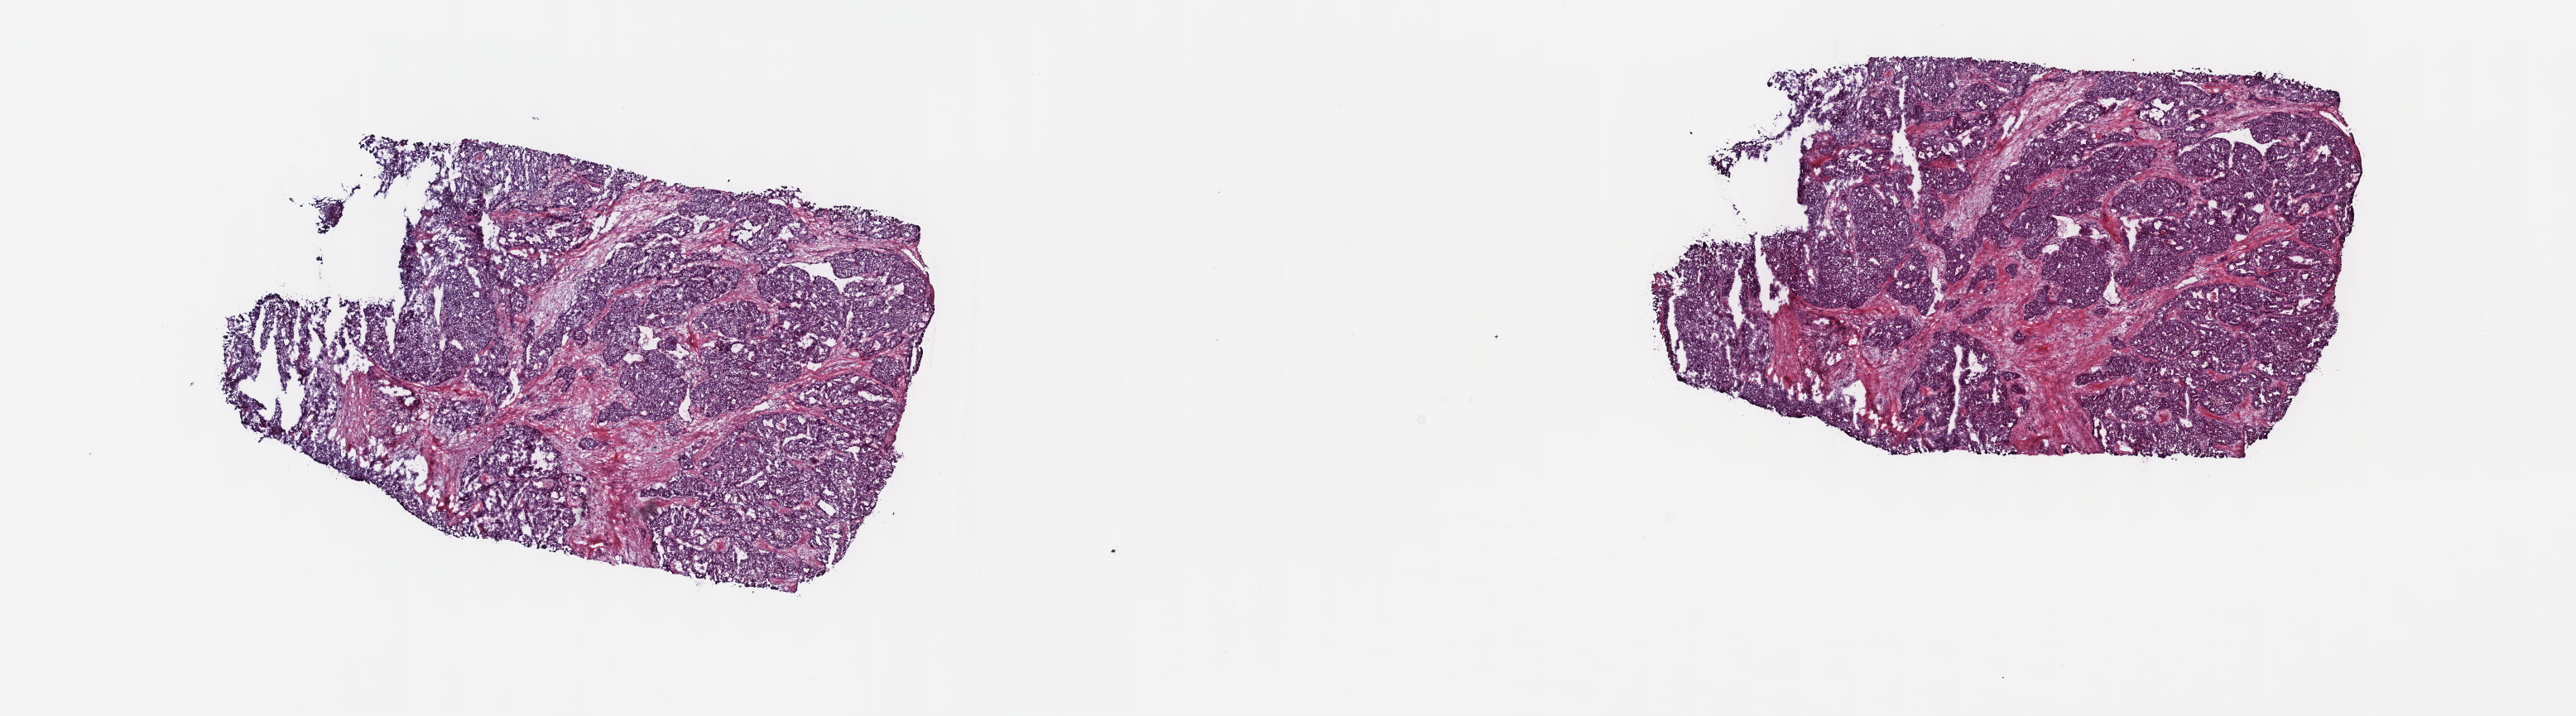
Digitized Hematoxylin and eosin (H&E) stained tissue section (whole slide), shown as a low-resolution overview of the whole scanned area (about 25.2 x 7.0 mm, acquisition: 40x scan). Frozen section from the top of the tissue portion. Liver, primary tumour sample. Female patient; age at initial diagnosis 51 years. Histologic grade: G2 (moderately differentiated). Slide review estimates, as recorded: tumour cells 100%, tumour nuclei 90%, normal cells 0%, stromal cells 0%, necrosis 0%. Inflammatory infiltration, as recorded: lymphocyte infiltration 0%, monocyte infiltration 0%, neutrophil infiltration 0%.
AJCC pathologic stage: II (6th edition). Diagnosis: Hepatocellular carcinoma, NOS. TNM: T2 N0 M0.